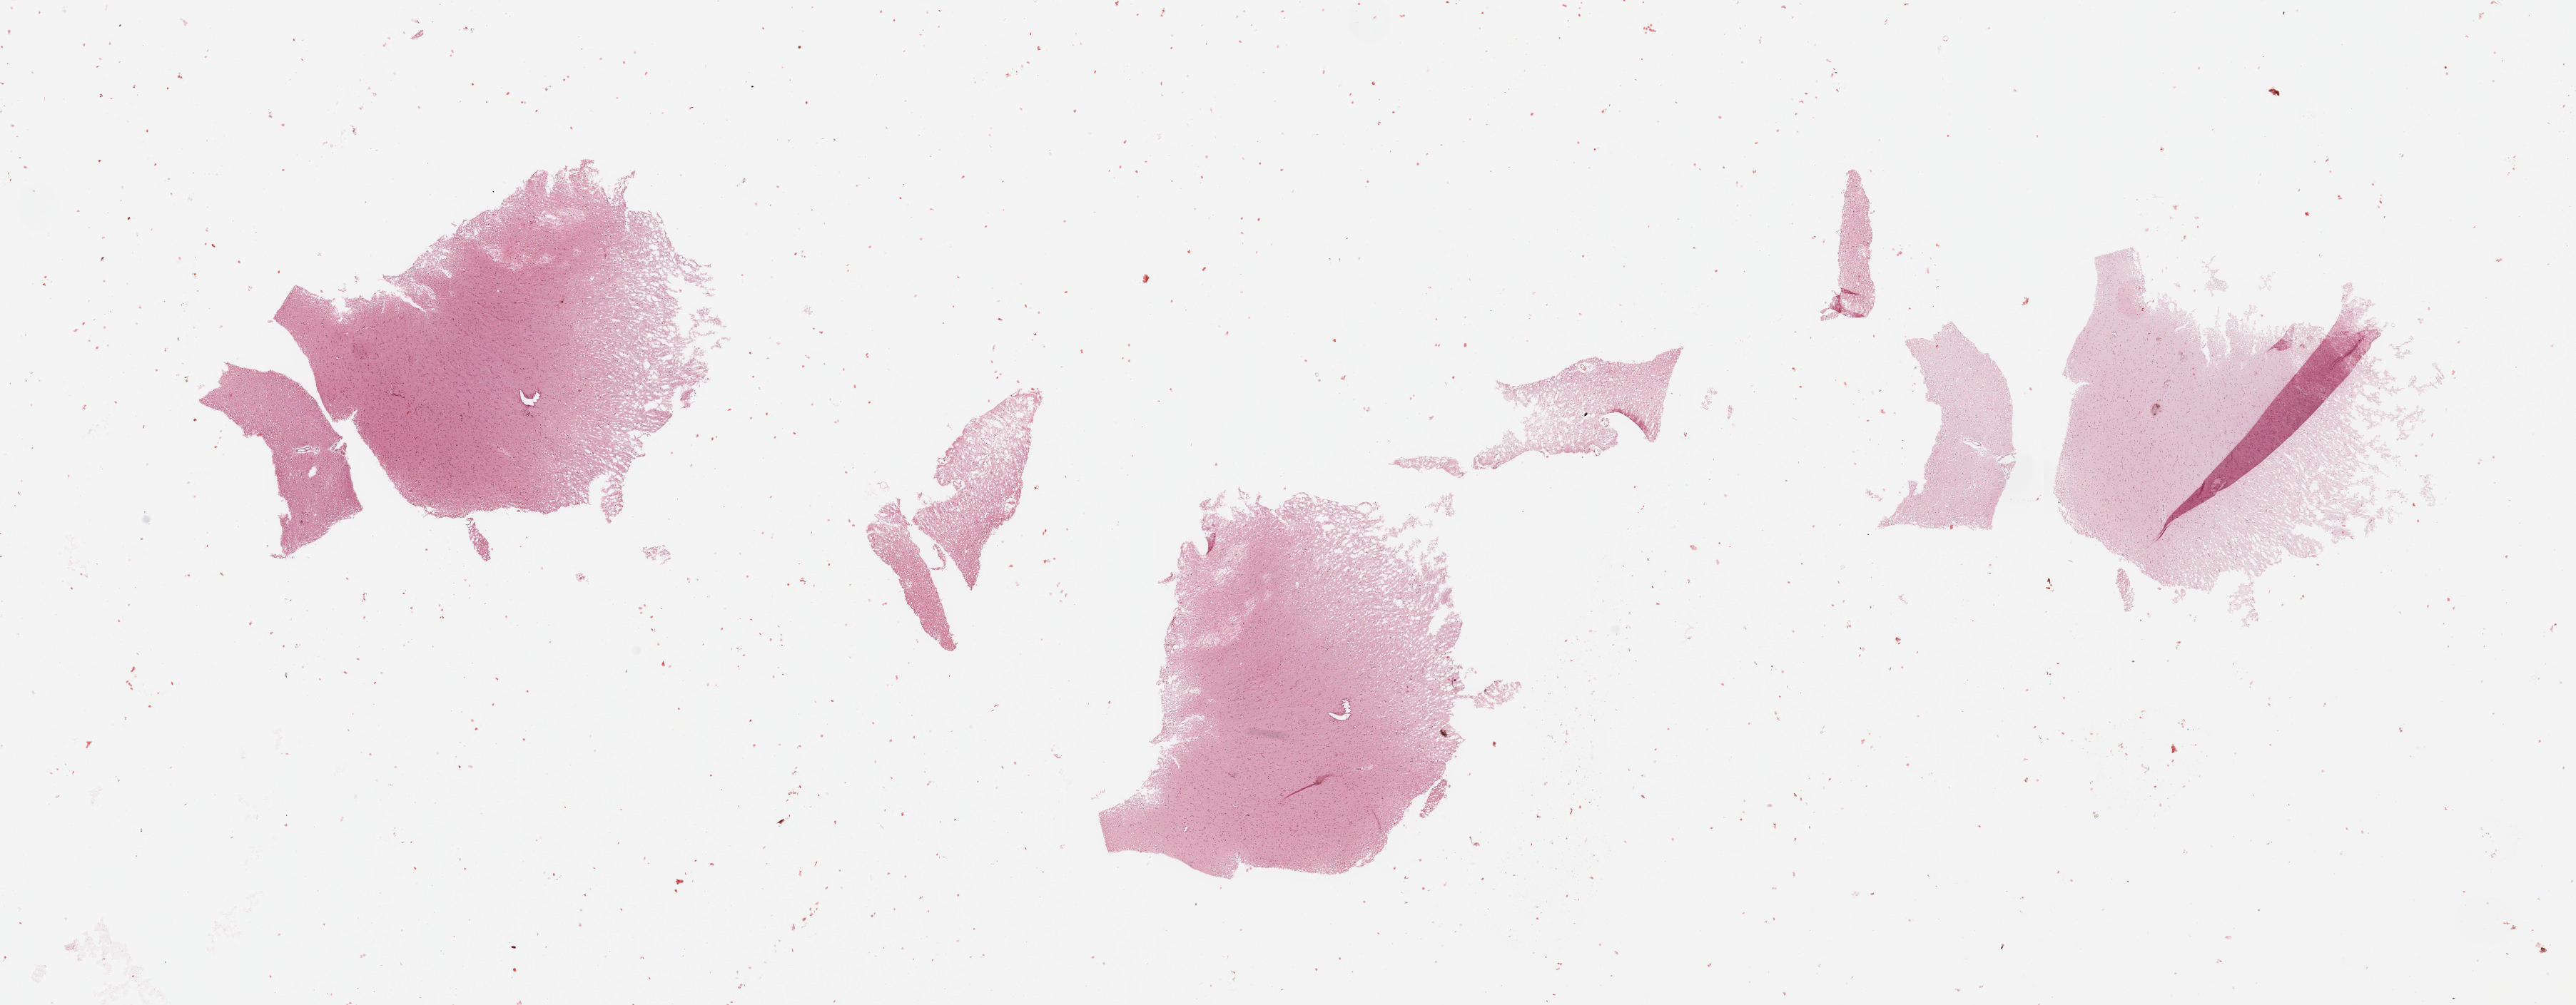
Whole-slide histology image, H&E — whole scanned area (about 28.5 x 11.1 mm) shown as a low-resolution overview, brain, tumour tissue. Female, 36 y/o.
Primary tumour site (as recorded): temporal lobe. Patient diagnosis (cohort enrolment): glioblastoma multiforme (brain).